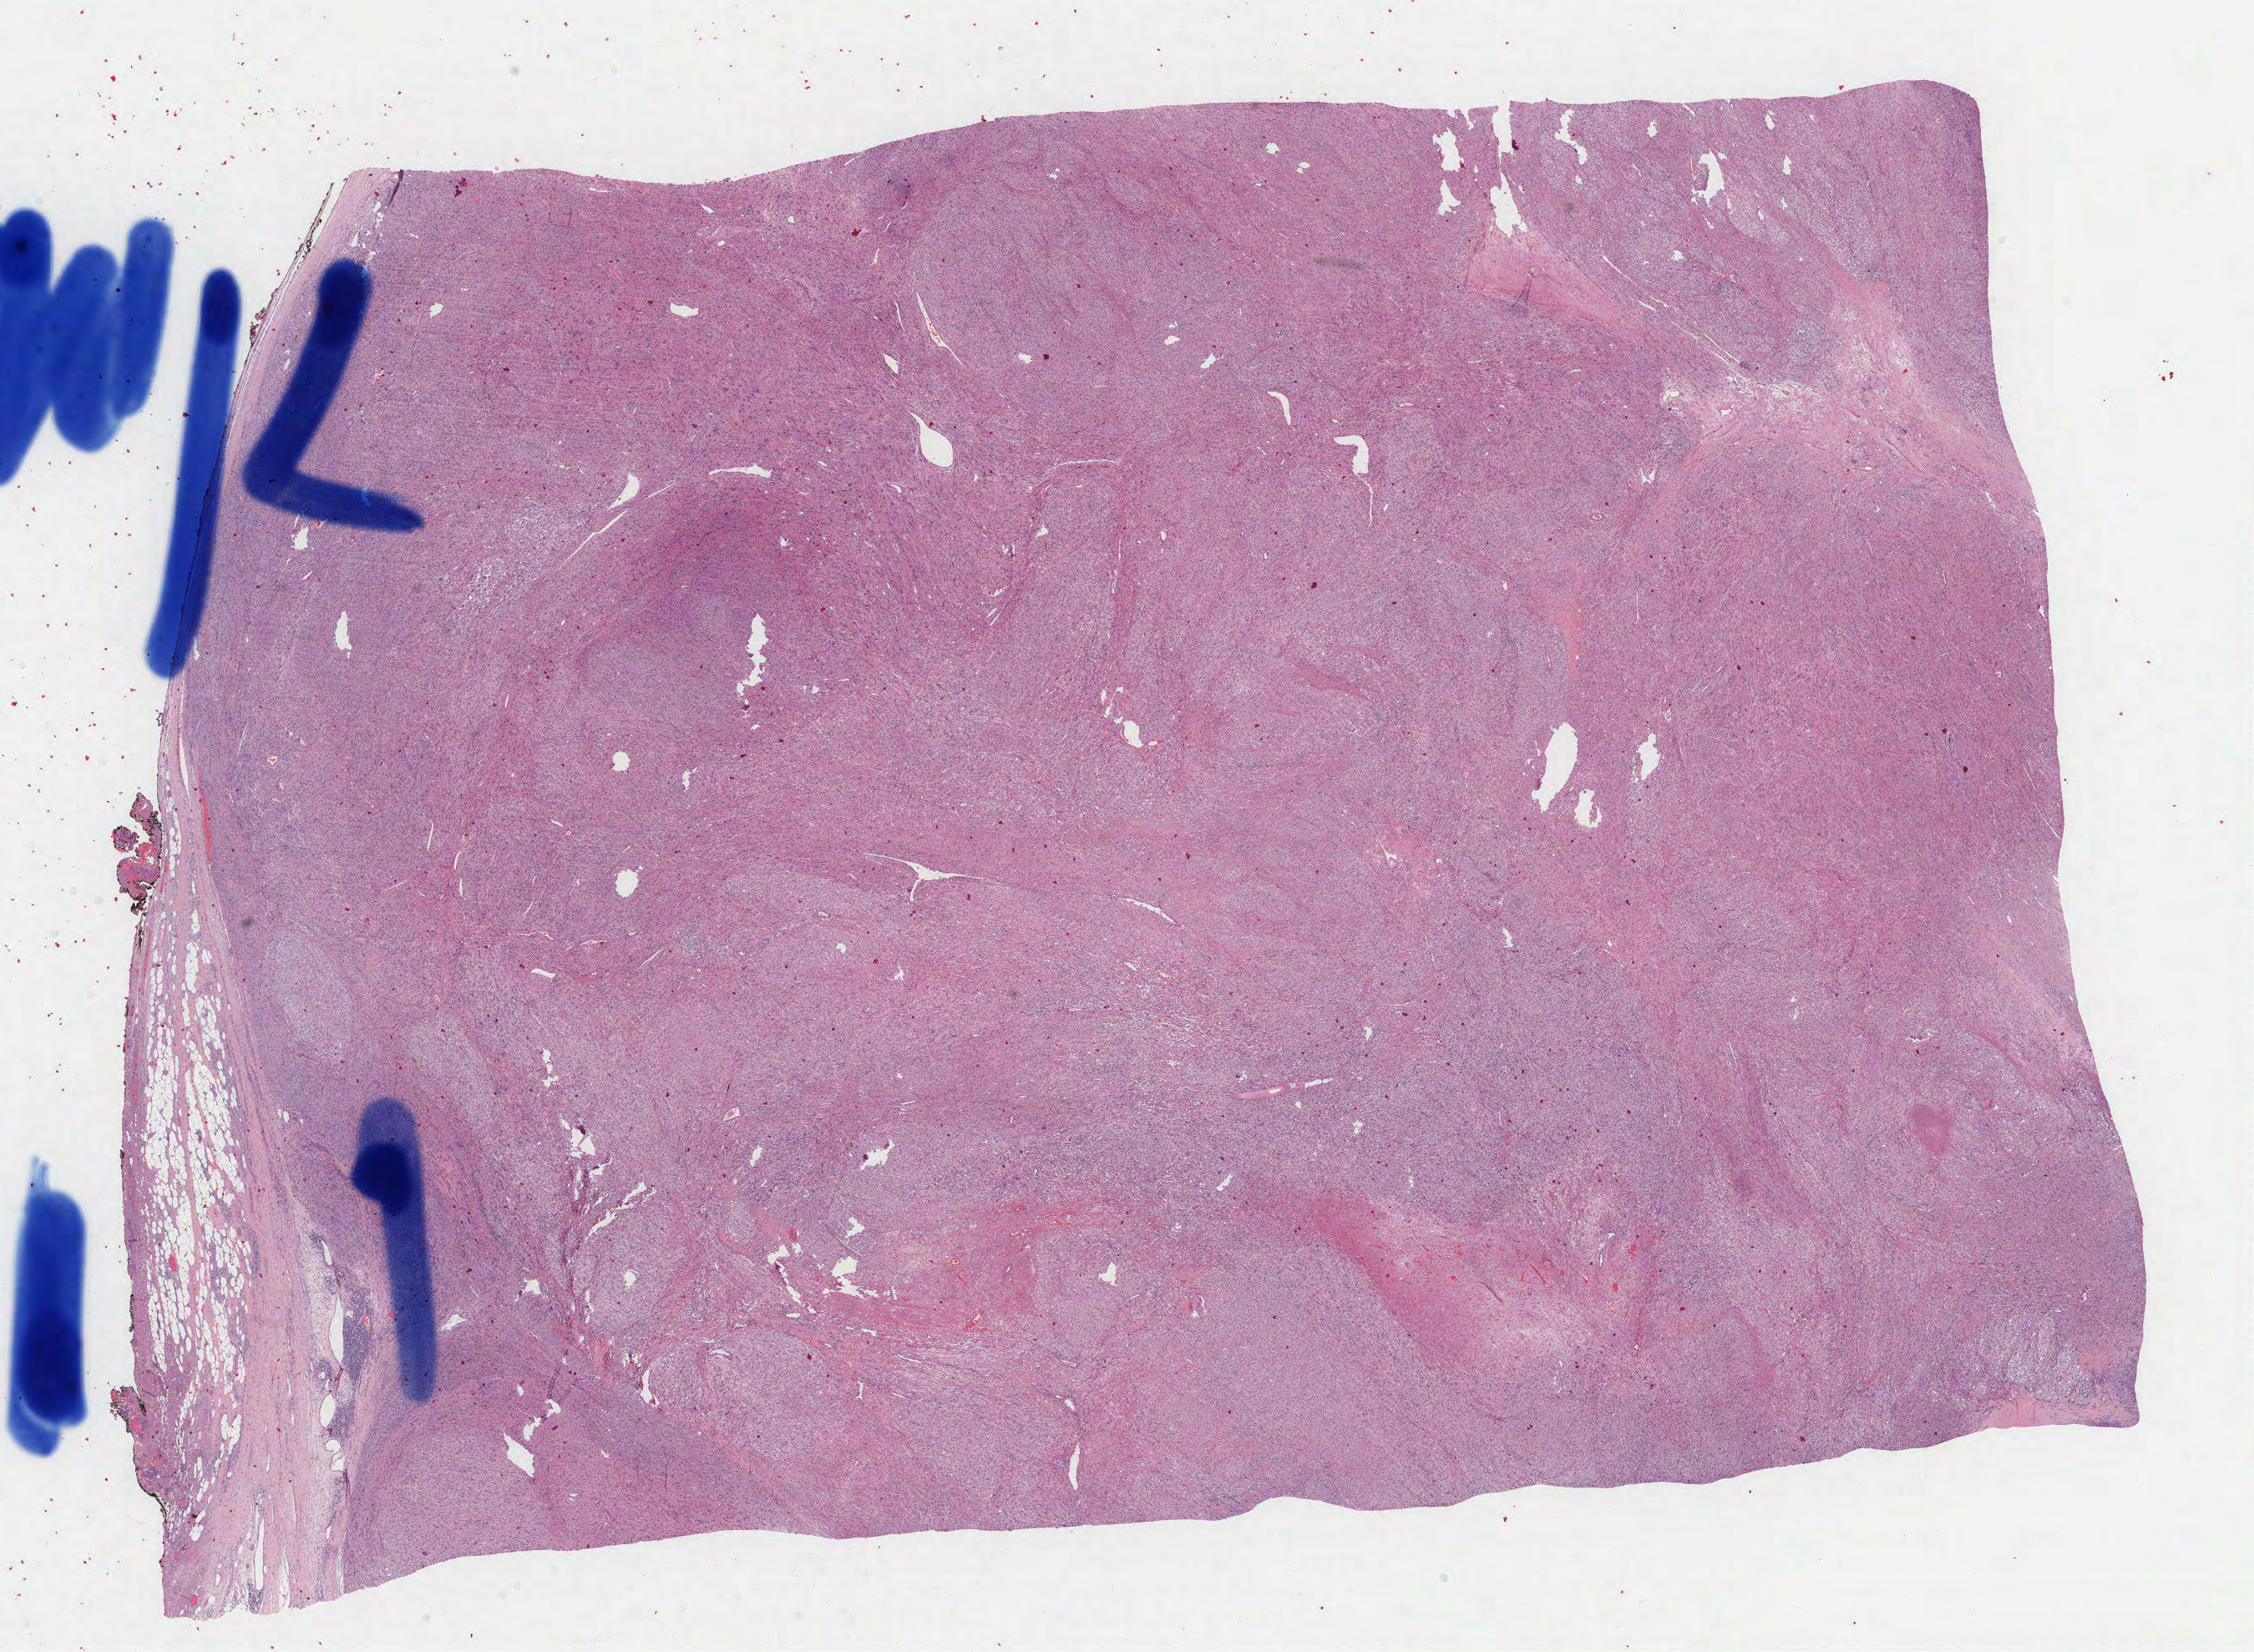
H&E-stained whole-slide image, whole scanned area (about 21.8 x 16.0 mm) shown as a low-resolution overview. FFPE section. Primary tumour sample from the connective, subcutaneous and other soft tissues. Male, age 66 years at initial diagnosis.
Pathologic diagnosis: Leiomyosarcoma, NOS (connective, subcutaneous and other soft tissues of thorax).